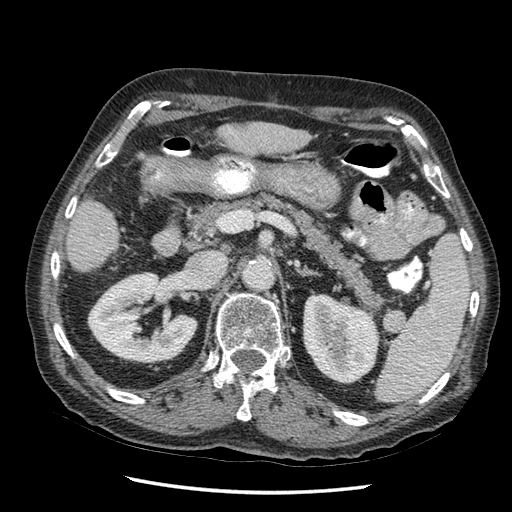
Contrast-enhanced abdominal CT (liver protocol), one axial slice. Position 16 of 67 along the scan axis. Reconstruction kernel STANDARD. 120 kVp. Soft-tissue window (W 400 / L 40 HU). 2.5 mm slice thickness. 512 × 512 image matrix, field of view 360 × 360 mm. From the clinical record (not read from this slice): diagnosis: hepatocellular carcinoma (patient treated with transarterial chemoembolisation; whether this scan precedes or follows treatment is not stated here); TNM stage (as recorded): Stage-I; Child-Pugh class: A; tumour nodularity: uninodular.
Annotated regions visible in this slice (semi-automatically segmented with operator editing):
- liver parenchyma outside the tumour (the mass and vessels are separate outlines, so this box may not span the whole liver): box from (x=206, y=118) to (x=316, y=162) px